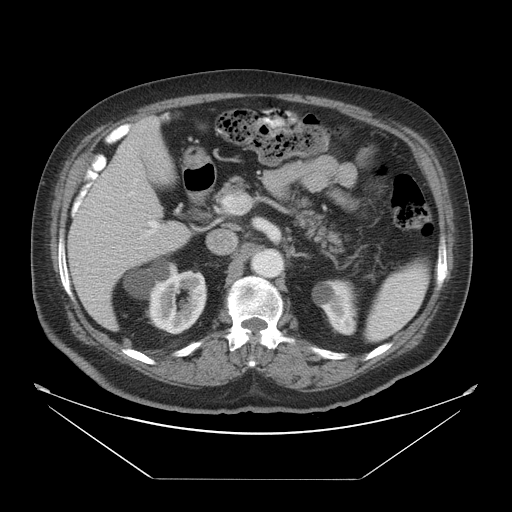
Contrast-enhanced abdominal CT, one axial slice; position 26 of 45 along the scan axis; intravenous contrast given; soft-tissue window (W 400 / L 40 HU); 5 mm slice thickness; 512 × 512 image matrix, field of view 463 × 463 mm. Male patient, age 87 years. Case-level facts recorded for this patient, not image findings: diagnosis: colorectal cancer liver metastases, imaged before liver resection; multiple liver metastases: no; largest metastasis: 4.5 cm; chemotherapy before resection: no.
Outlined on this slice (manually delineated by an expert):
- liver: bounding box (x1, y1, x2, y2) in pixels: (68, 118, 191, 331)
- planned liver remnant (the part of the liver to remain after resection): (127, 118, 164, 149)
- portal vein (with intrahepatic branches): (131, 192, 164, 237)